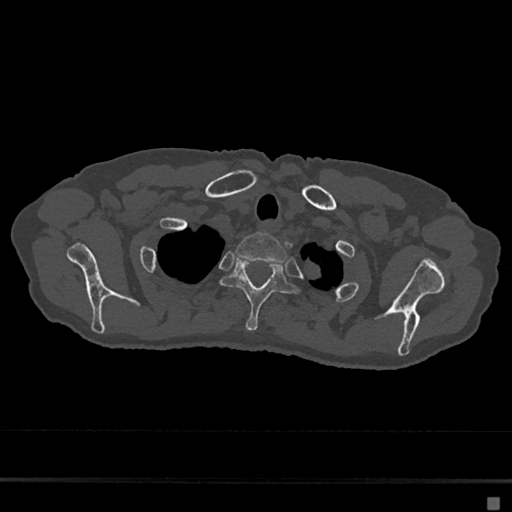
CT including the spine, one axial slice. Slice 582 of 797 in the series (ordered by position). Reconstruction kernel Br40s/3. 120 kVp. Bone window (W 1800 / L 400 HU). 512 × 512 image matrix. Patient: female, 68 years. Case-level facts recorded for this patient, not image findings: primary cancer: renal.
Outlined on this slice (semi-automatic segmentation, software-assisted and operator-edited):
- T1 vertebra: bounding box (x1, y1, x2, y2) in pixels: (236, 232, 287, 263)
- T2 vertebra: (220, 256, 296, 332)